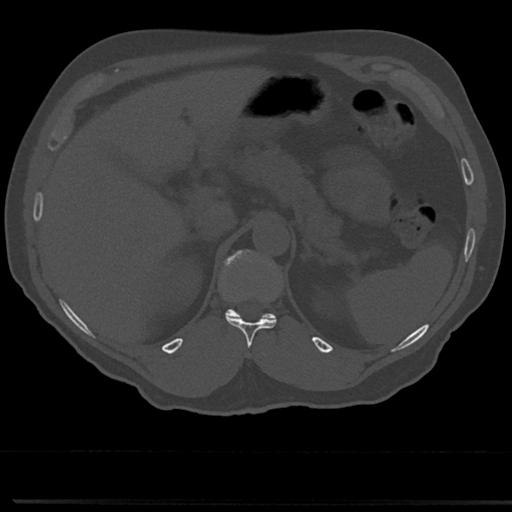
CT including the spine, one axial slice; slice 180 of 817 in the series (ordered by position); reconstruction kernel Br40s/3; 120 kVp; bone window (W 1800 / L 400 HU); 0.5 mm slice thickness; 512 × 512 image matrix. Patient: male, 61 years. Case-level facts recorded for this patient, not image findings: primary cancer: prostate.
Outlined on this slice (semi-automatically segmented with operator editing):
- T11 vertebra: bounding box (x1, y1, x2, y2) in pixels: (226, 317, 277, 349)
- T12 vertebra: (221, 250, 276, 321)